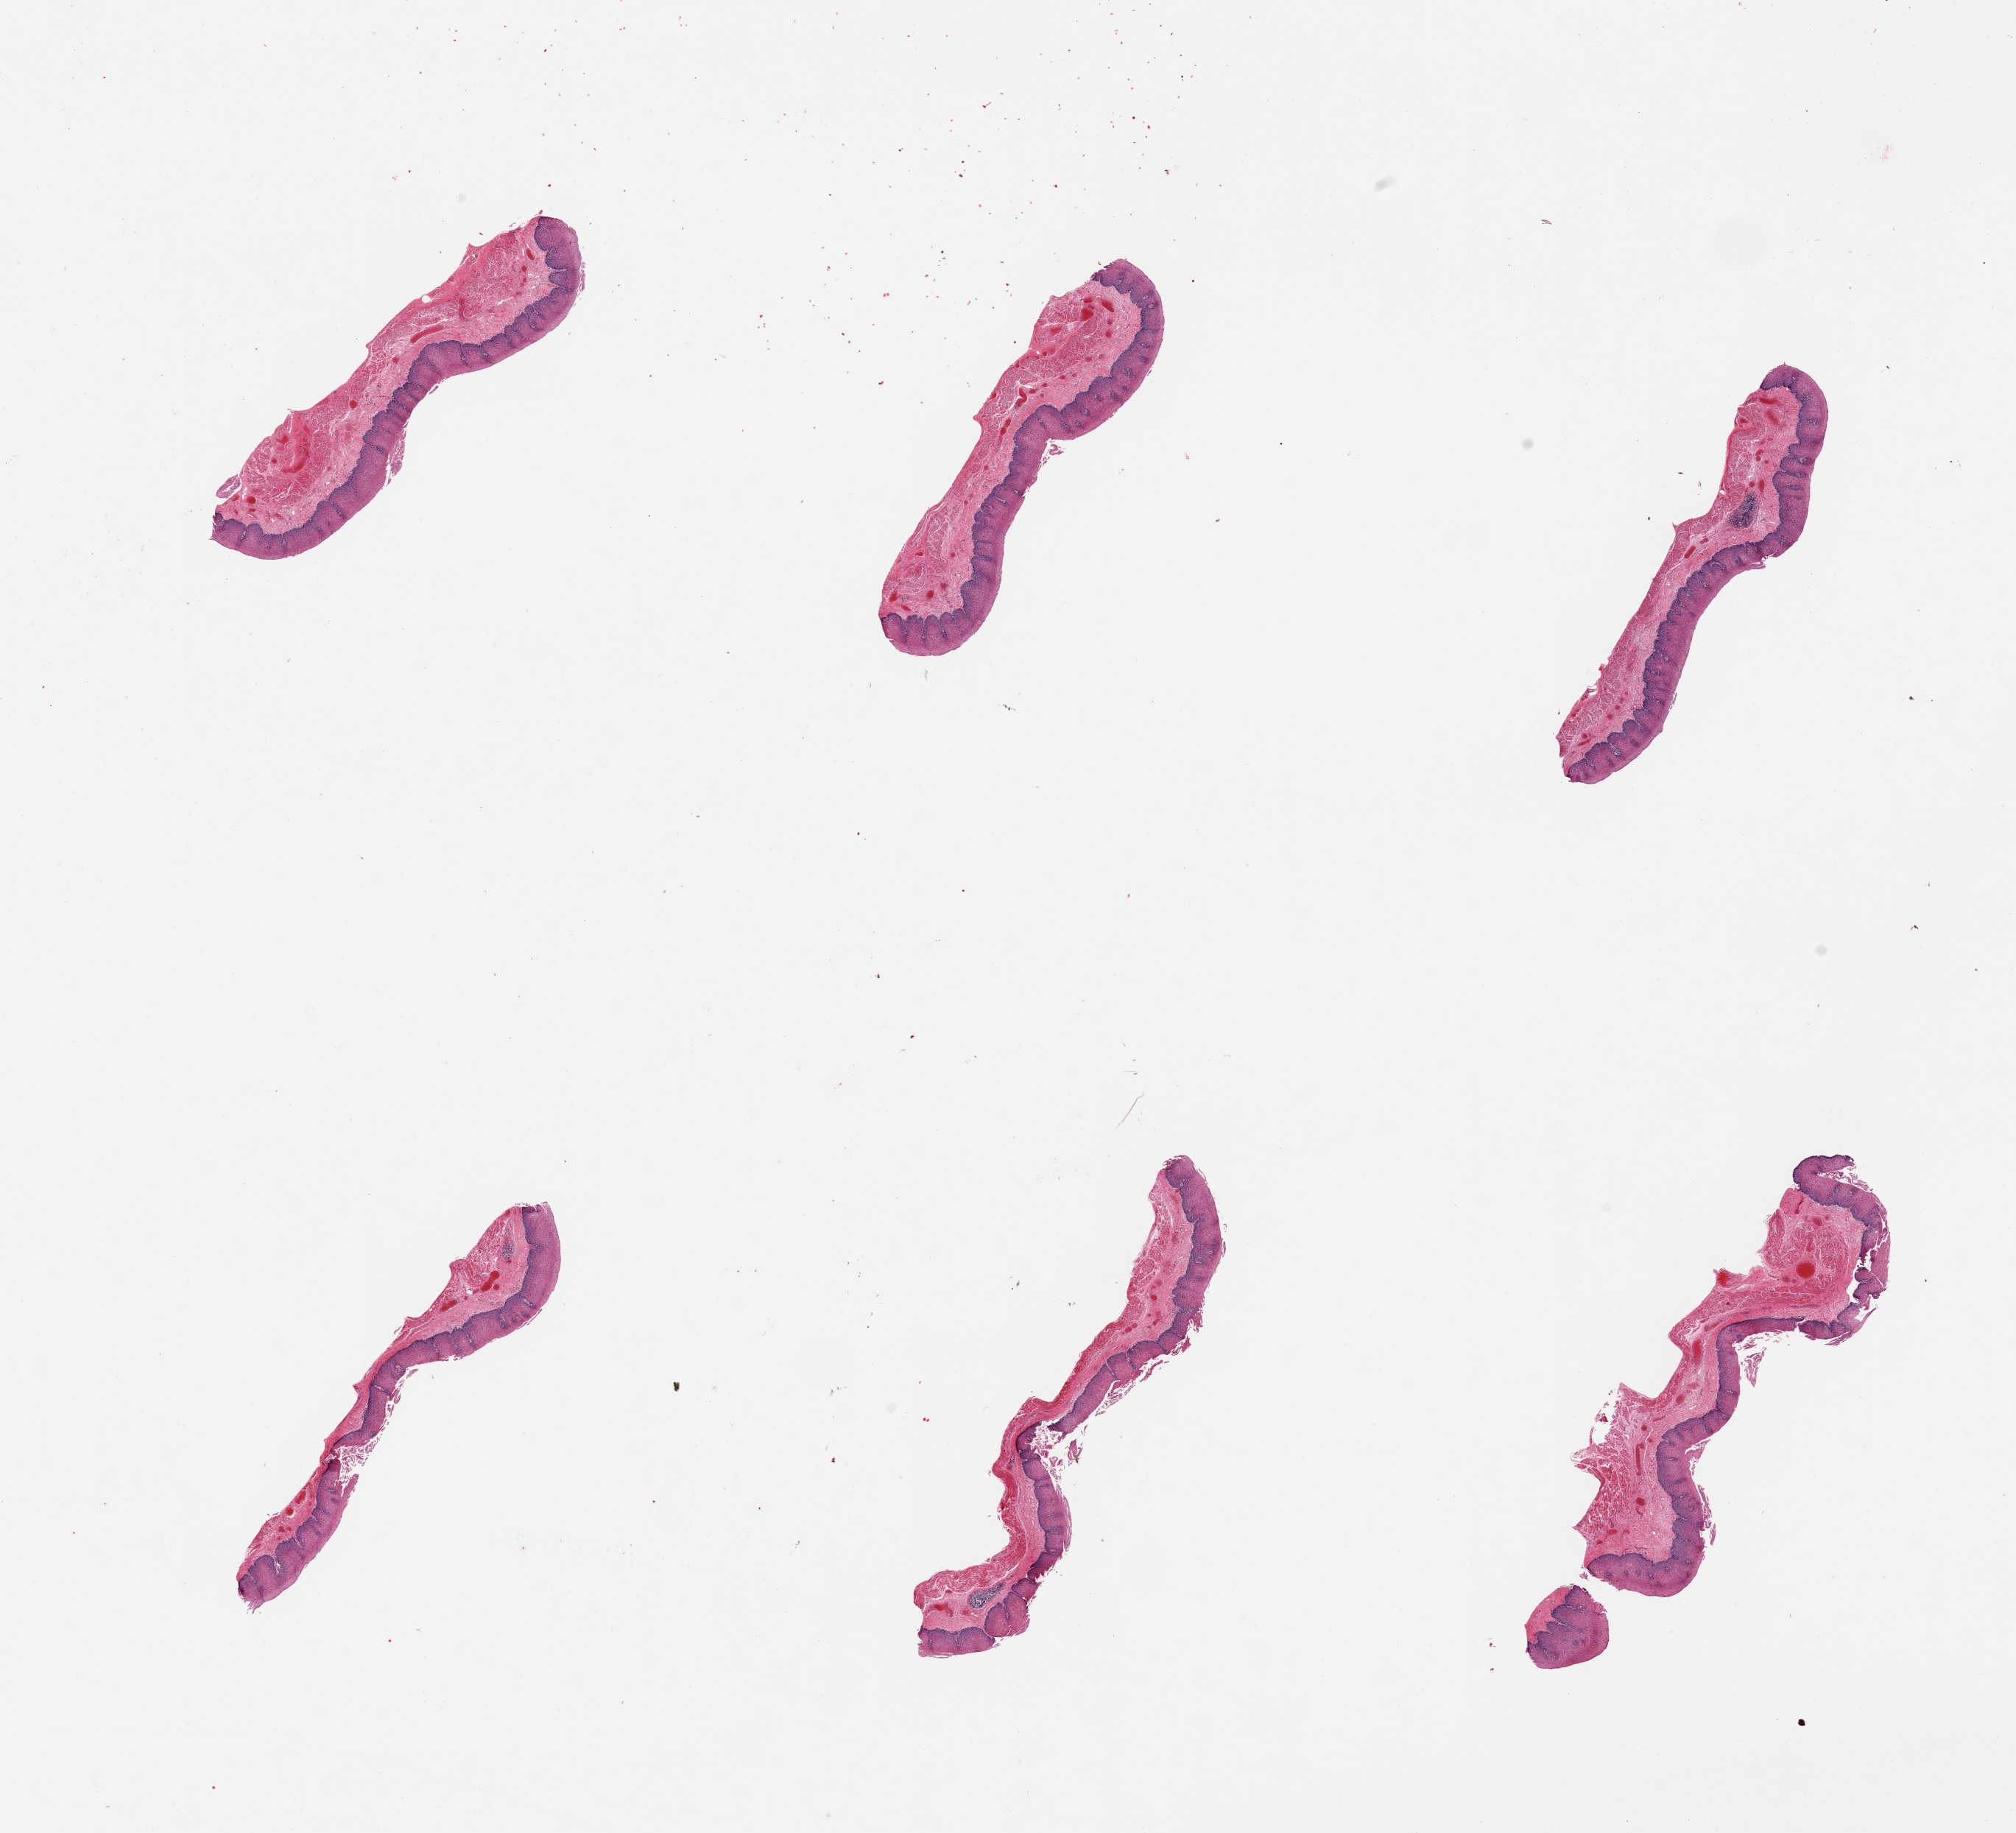
Whole-slide image, H&E stain — a low-resolution overview of the entire scanned area, about 21.7 x 19.7 mm. PAXgene-fixed paraffin-embedded (PFPE) section. Section of esophageal mucous membrane (target tissue). Donor tissue sample. Donor: male.
Reviewer comment on this tissue sample: 6 pieces. Hypertrophic epithelium (up to 0.3mm).